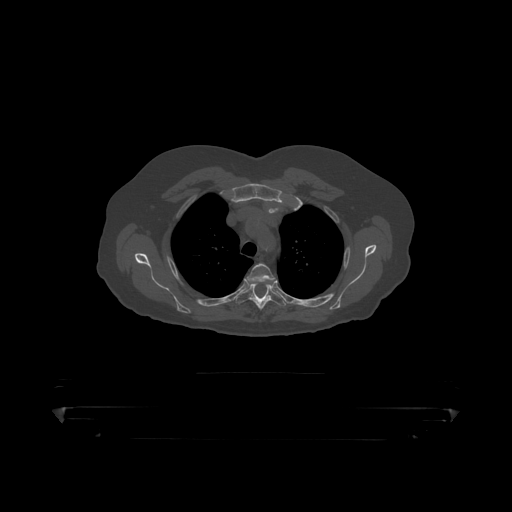
CT including the spine, one axial slice. Reconstruction kernel STANDARD. 120 kVp. Bone window (W 1800 / L 400 HU). 1.25 mm slice thickness. 512 × 512 image matrix, field of view 650 × 650 mm. Male patient, age 60 years. Case-level facts recorded for this patient, not image findings: primary cancer: prostate.
Structures marked on this image (semi-automatically segmented with operator editing):
- T3 vertebra: bounding box (x1, y1, x2, y2) in pixels: (247, 264, 276, 287)
- T4 vertebra: (236, 284, 286, 311)